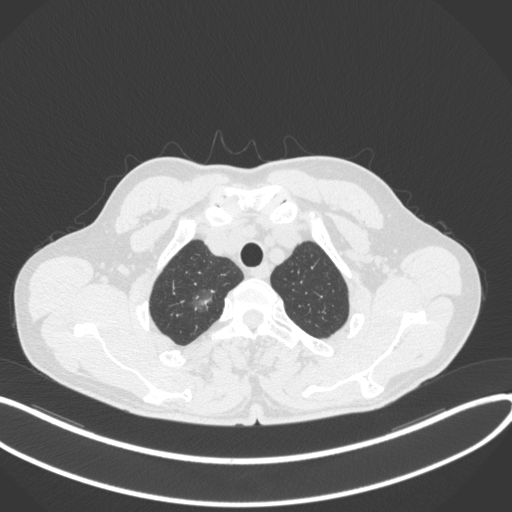
Chest CT, one axial slice; slice 337 of 407 in the series (ordered by position); reconstruction kernel B31f; lung window (W 1500 / L -600 HU); 1 mm slice thickness; 512 × 512 image matrix, field of view 400 × 400 mm. Patient: male, 58 years. From the clinical record (not read from this slice): clinical TNM (as recorded): T1c N0 M0; histopathological grade: G1-2.
Annotated regions visible in this slice (bounding box drawn by a radiologist):
- lung tumour (recorded histology: adenocarcinoma): bounding box (x1, y1, x2, y2) in pixels: (183, 285, 218, 314)